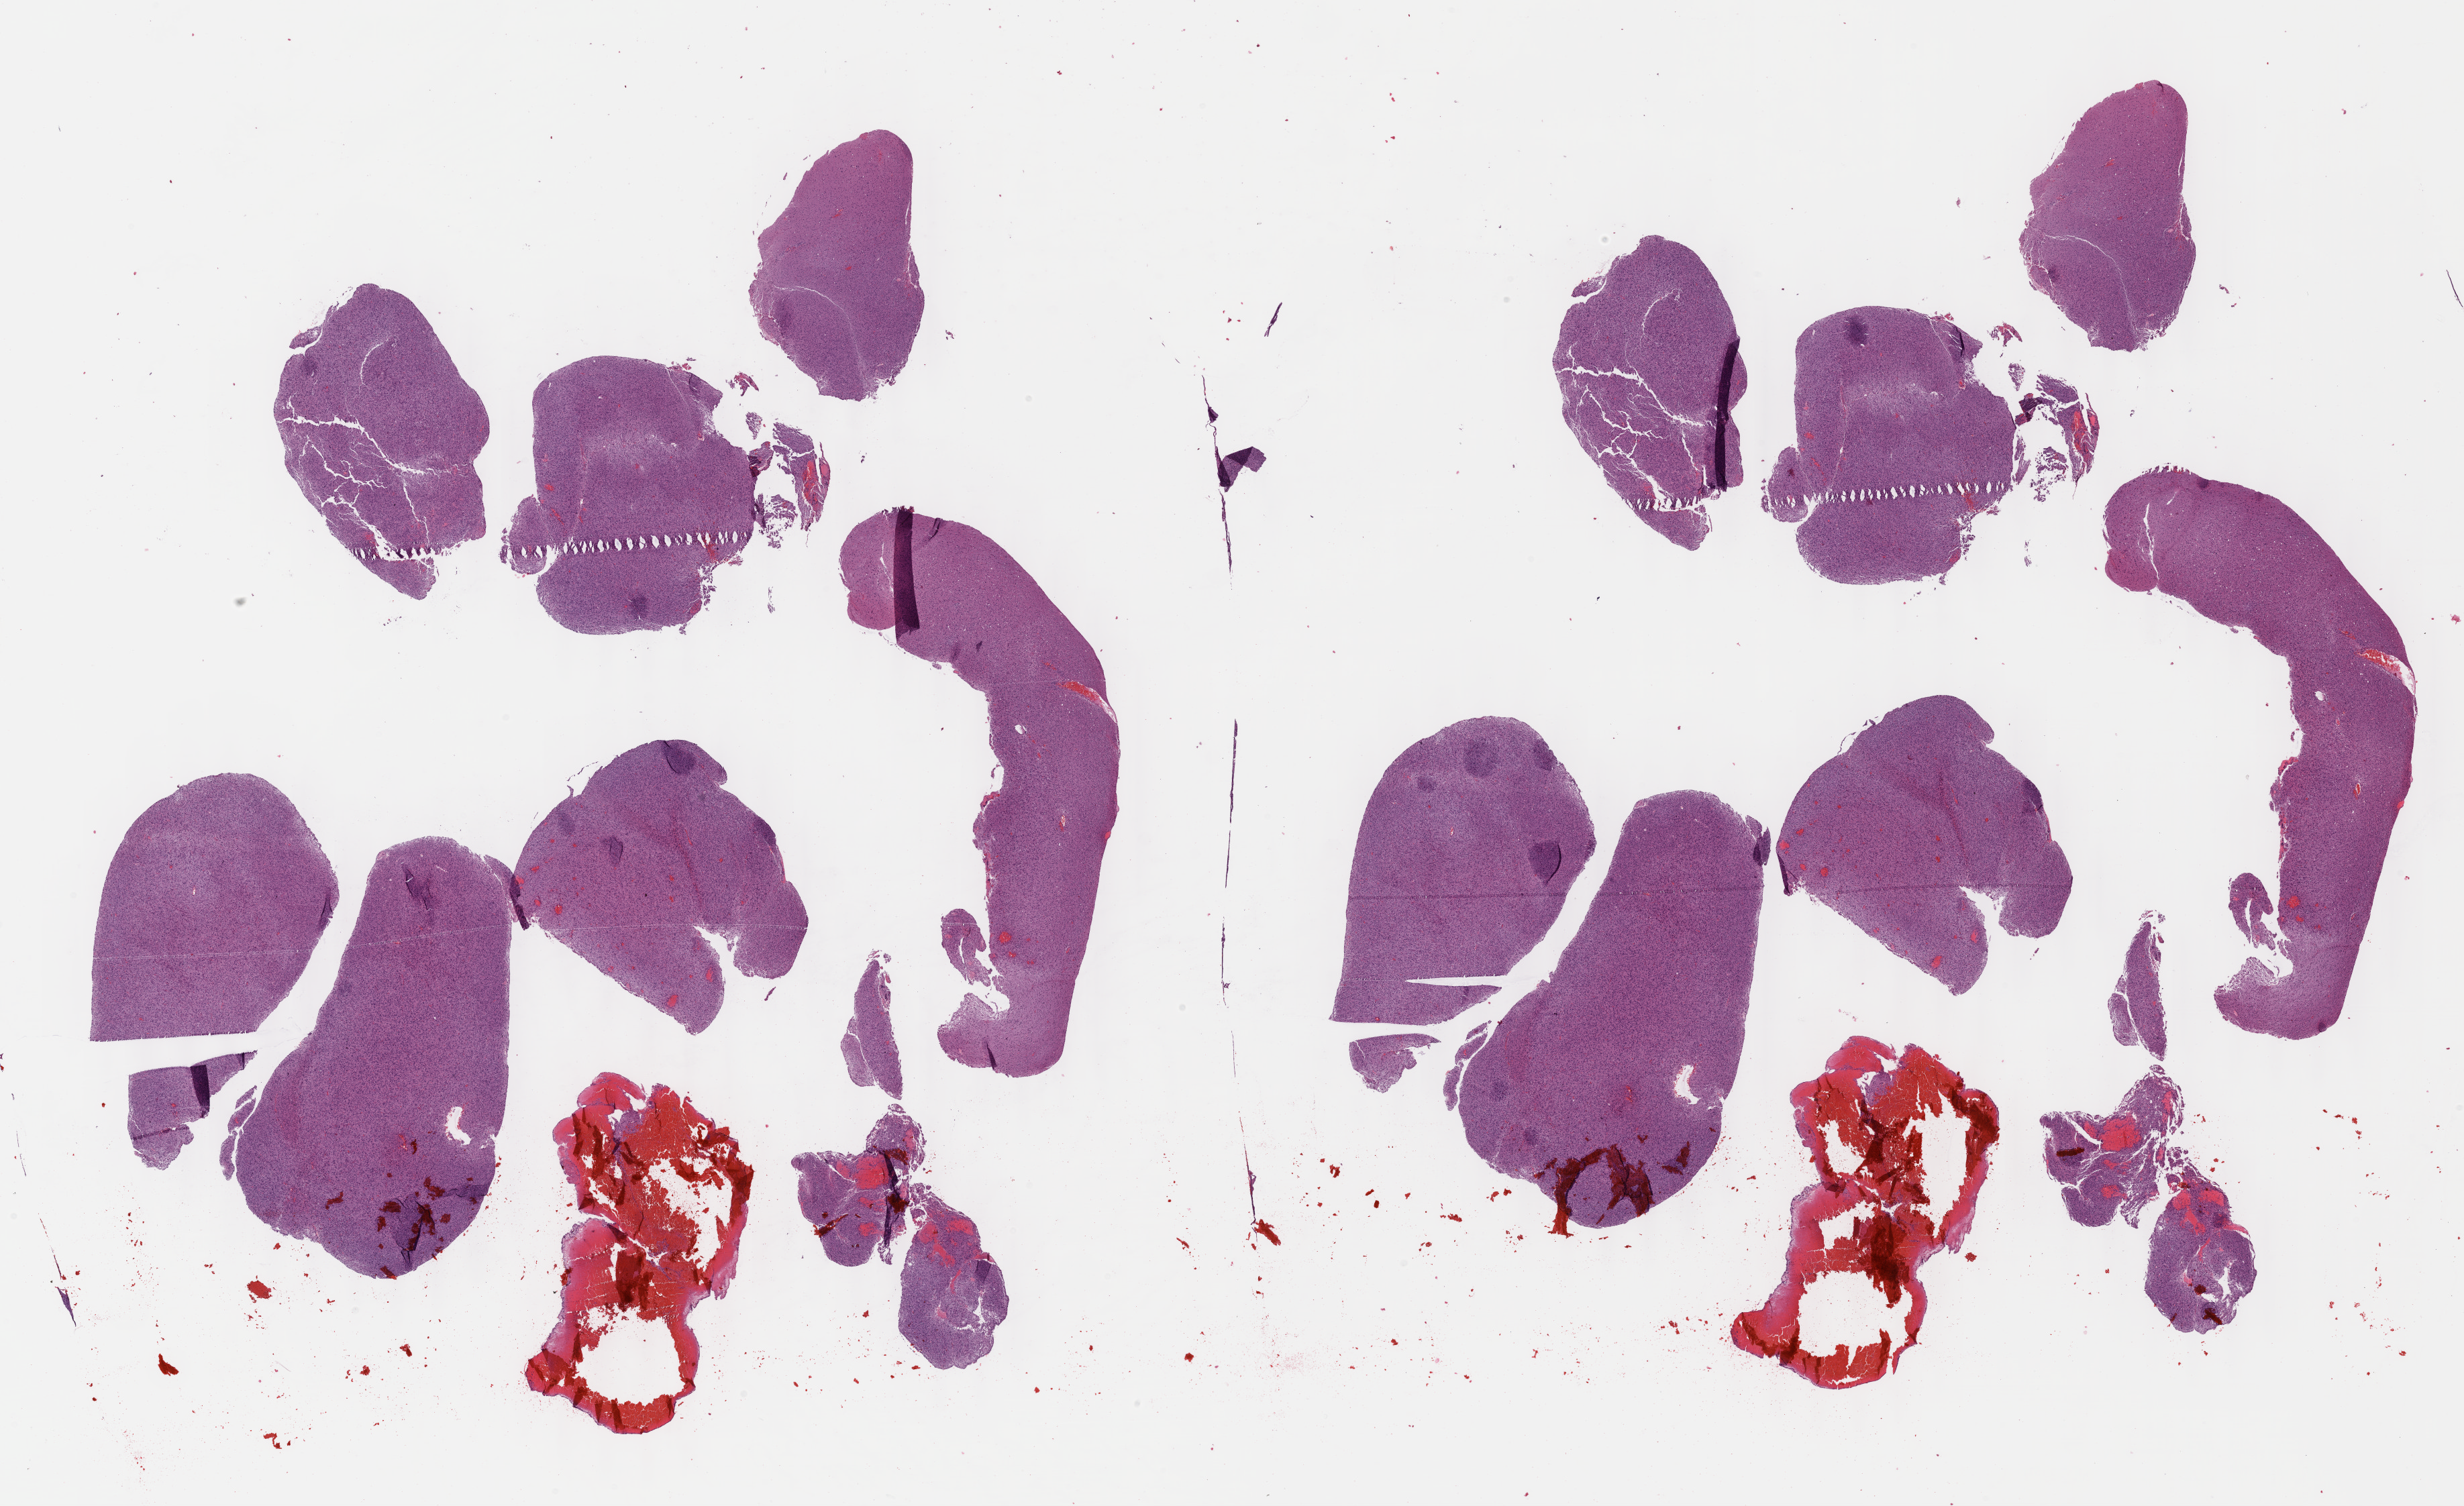
H&E whole-slide image, shown as a low-resolution overview of the whole scanned area (about 29.7 x 18.1 mm); formalin-fixed paraffin-embedded (FFPE) diagnostic section; primary tumour sample from the brain. Female, age 65 years at initial diagnosis. Histologic grade: G3 (poorly differentiated).
- diagnosis: Astrocytoma, anaplastic (cerebrum)